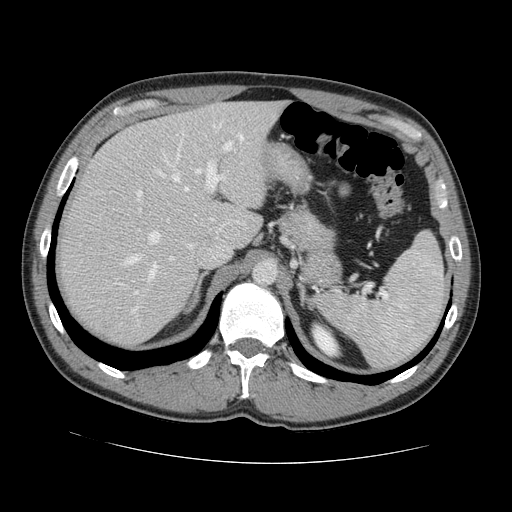
Contrast-enhanced abdominal CT, one axial slice. Position 94 of 131 along the scan axis. Intravenous contrast given. Soft-tissue window (W 400 / L 40 HU). 512 × 512 image matrix, field of view 380 × 380 mm. Male patient, age 40 years. From the clinical record (not read from this slice): diagnosis: colorectal cancer liver metastases, imaged before liver resection; multiple liver metastases: yes; largest metastasis: 2.9 cm.
Structures marked on this image (outlined manually by an expert reader):
- hepatic veins: box from (x=126, y=136) to (x=243, y=313) px
- liver: (x=61, y=102)–(x=282, y=346)
- planned liver remnant (the part of the liver to remain after resection): (x=99, y=102)–(x=283, y=246)
- portal vein (with intrahepatic branches): (x=133, y=141)–(x=233, y=295)